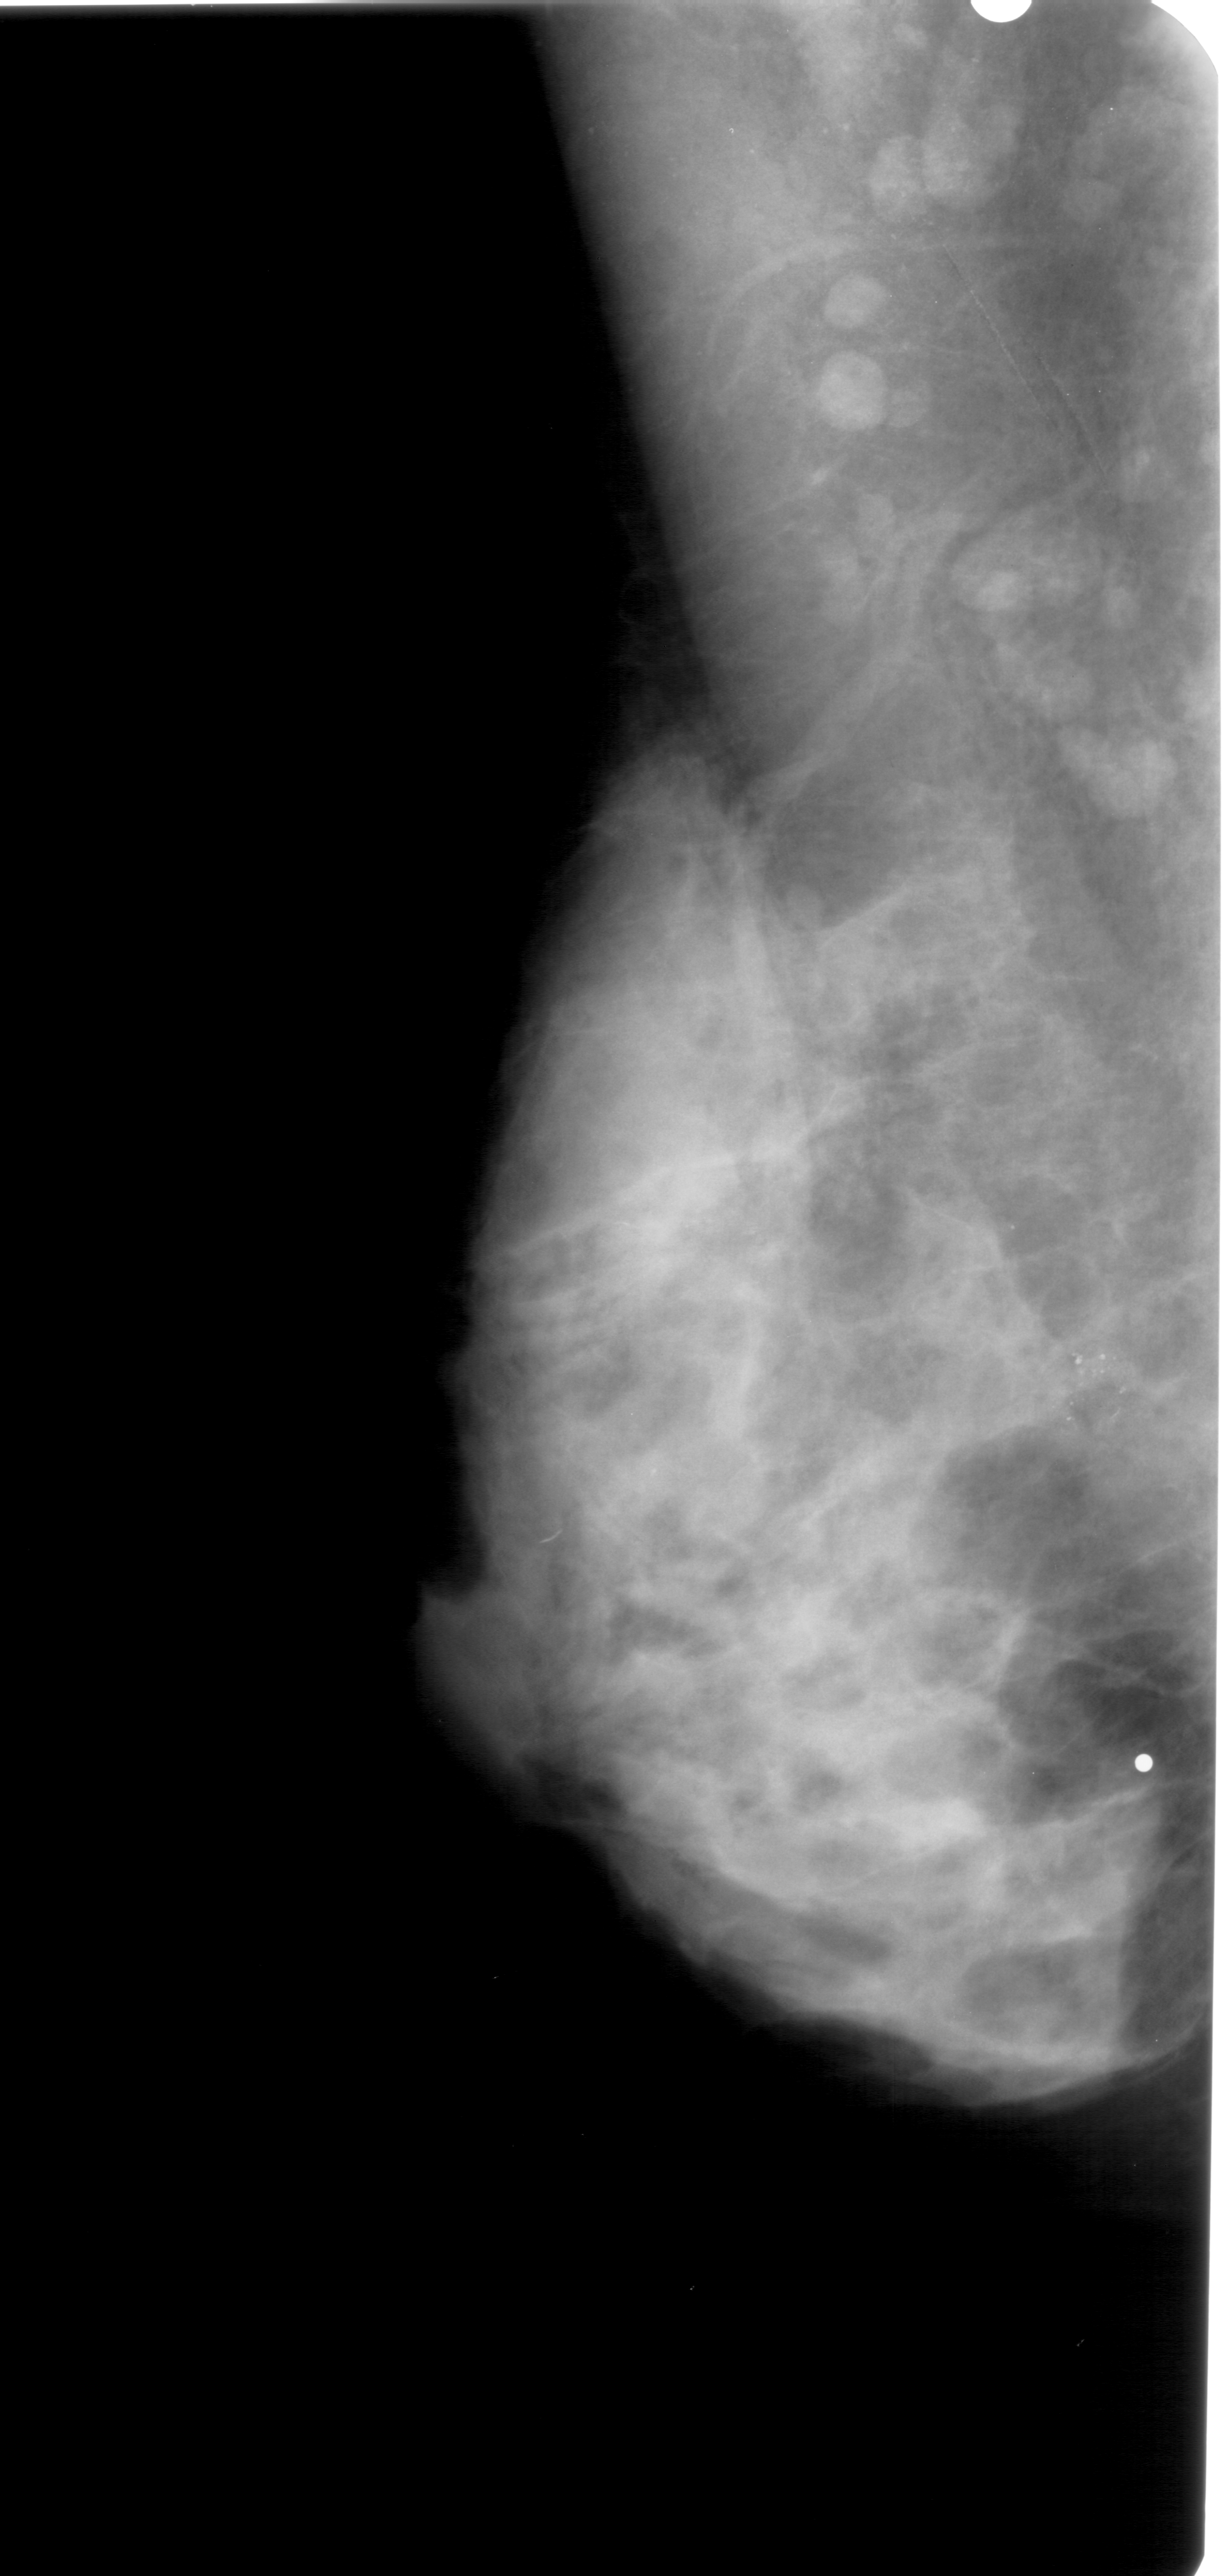
Scanned film-screen mammogram, left breast, MLO view.
- Marked findings (only marked abnormalities are described; nothing is implied about the rest of the image): calcifications, morphology pleomorphic, distribution clustered; BI-RADS assessment category 4; subtlety rating 4 on a 1 (subtle) to 5 (obvious) scale; pathology (as recorded): benign.